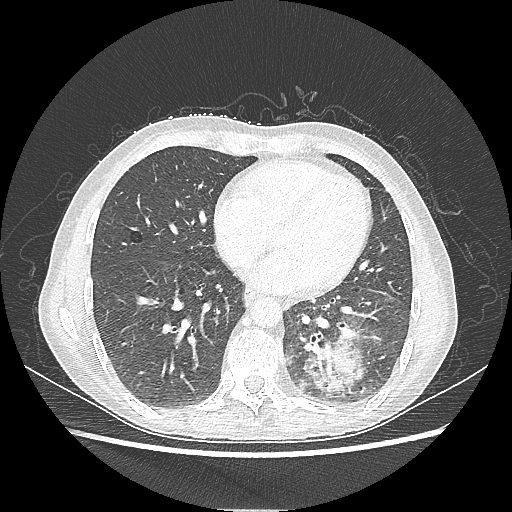
Chest CT, one axial slice; slice 85 of 220 in the series (ordered by position); reconstruction kernel LUNG; lung window (W 1500 / L -600 HU); 1.25 mm slice thickness; 512 × 512 image matrix, field of view 360 × 360 mm. Patient: female, 53 years. From the clinical record (not read from this slice): clinical TNM (as recorded): T3 N0 M0.
Annotated regions visible in this slice (bounding box drawn by a radiologist):
- lung tumour (recorded histology: adenocarcinoma): box from (x=305, y=336) to (x=365, y=395) px